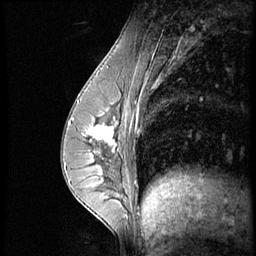
Breast MRI (dynamic contrast-enhanced), one sagittal slice; position 24 of 56 along the scan axis; dynamic contrast-enhanced series, image 2 of 4 at this slice position (ordered by acquisition); 1.5 T; TE 4.2 ms, TR 8.9 ms; 2.5 mm slice thickness; 256 × 256 image matrix. Patient: female, 35 years. Case-level facts recorded for this patient, not image findings: setting: breast cancer imaged before/during neoadjuvant chemotherapy; receptor status: HER2-positive.
Outlined on this slice (semi-automatically segmented with operator editing):
- analysis volume of interest (the breast-tissue region the enhancement analysis was run in; not a lesion): box from (x=73, y=111) to (x=131, y=164) px
- tumour enhancement mask (voxels above the 140 % enhancement threshold inside the analysis volume of interest): (x=79, y=121)–(x=118, y=154)